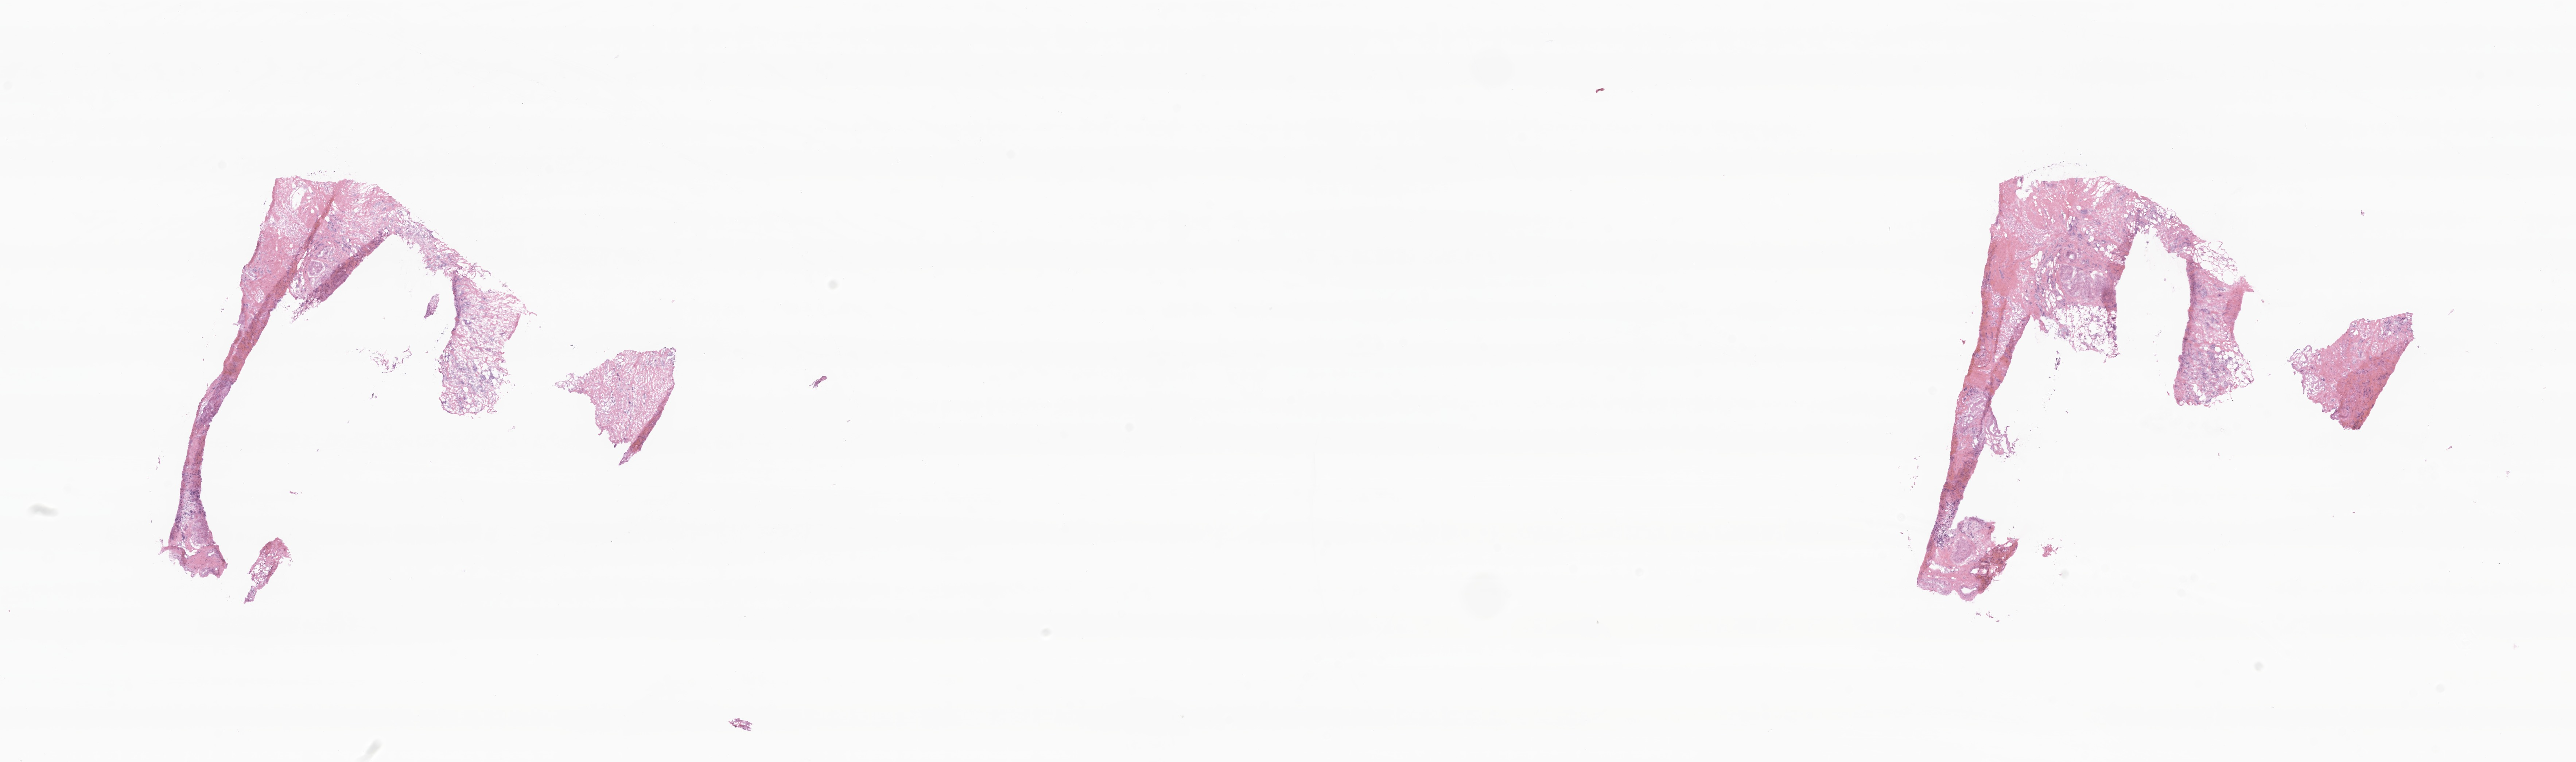
Whole-slide image, haematoxylin and eosin stain, a low-resolution overview of the entire scanned area, about 29.8 x 8.8 mm; cryosection; specimen: primary tumor; site: breast (left). Patient: female, age at initial diagnosis 51 years. Composition of this section per pathologist review: tumor cells 17%, tumor nuclei 80%, stromal cells 82%, necrosis 1%, normal cells 0%. Infiltration values recorded for this section: lymphocyte infiltration 10%, monocyte infiltration 0%, neutrophil infiltration 0%.
- histologic diagnosis: Infiltrating duct carcinoma, NOS
- section: bottom of the tissue portion